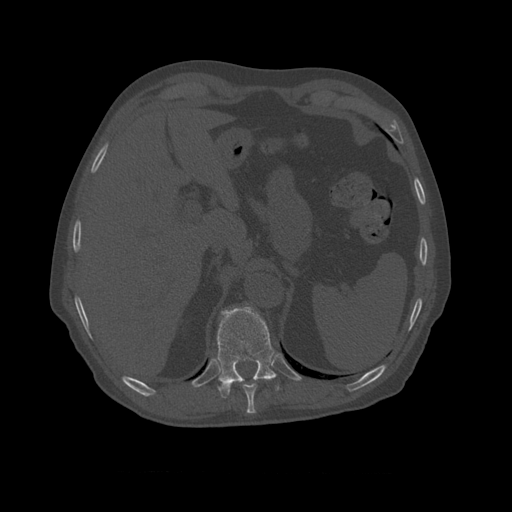
CT including the spine, one axial slice. Slice 408 of 450 in the series (ordered by position). 120 kVp. Bone window (W 1800 / L 400 HU). 1.25 mm slice thickness. 512 × 512 image matrix. Patient age 75 years. From the clinical record (not read from this slice): primary cancer: prostate.
Annotated regions visible in this slice (semi-automatically segmented with operator editing):
- T10 vertebra: box from (x=217, y=306) to (x=280, y=398) px
- T9 vertebra: (x=243, y=383)–(x=258, y=410)